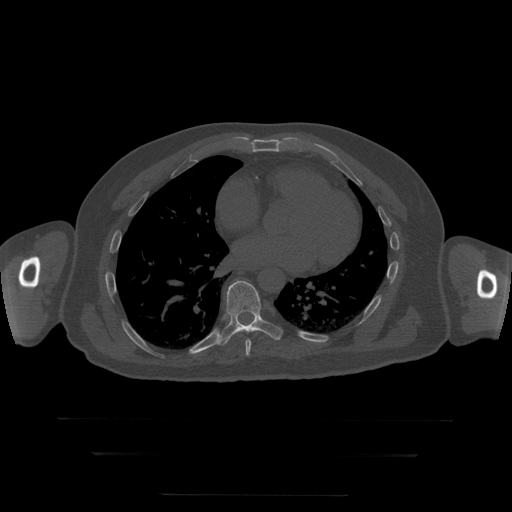
CT including the spine, one axial slice. Bone window (W 1800 / L 400 HU). 1.25 mm slice thickness. 512 × 512 image matrix, field of view 510 × 510 mm. Patient age 73 years. Case-level facts recorded for this patient, not image findings: primary cancer: prostate.
Outlined on this slice (semi-automatic segmentation, software-assisted and operator-edited):
- T8 vertebra: box from (x=246, y=340) to (x=252, y=357) px
- T9 vertebra: (x=217, y=281)–(x=283, y=346)